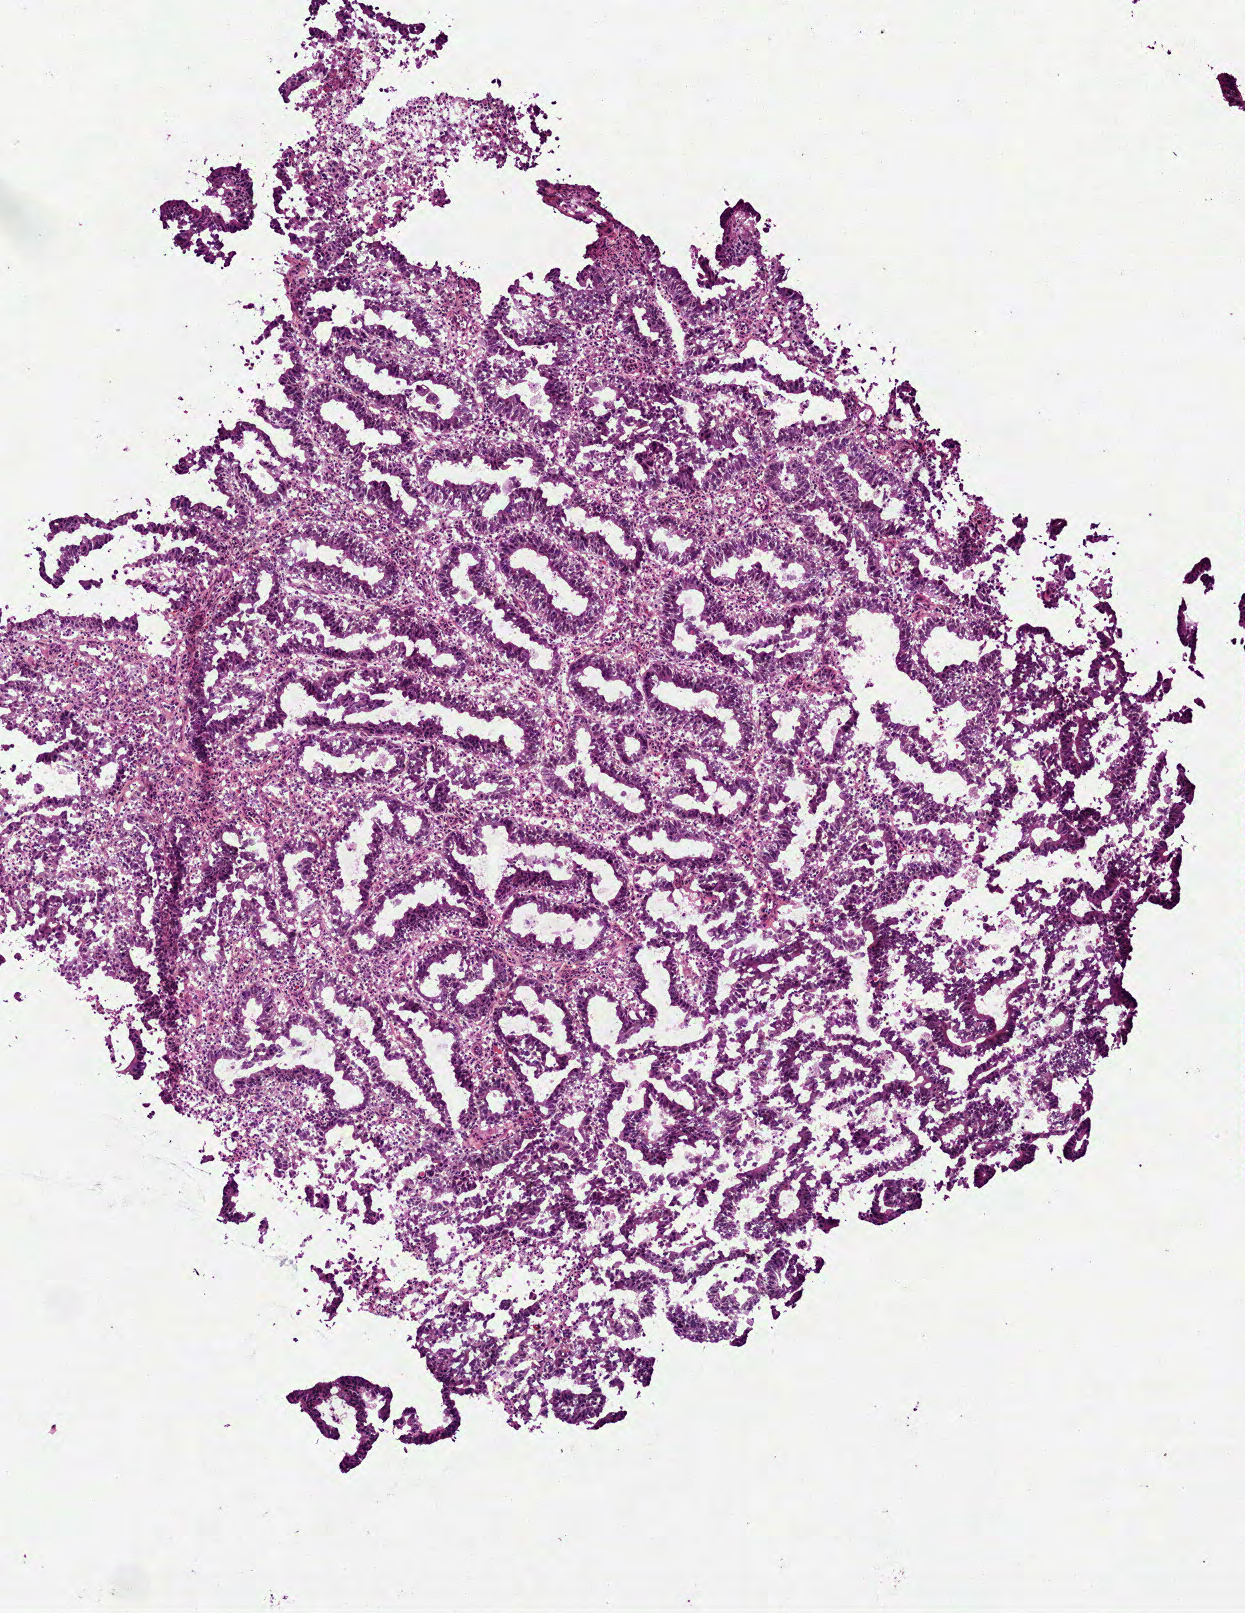
Whole-slide histology image, H&E-stained — shown as a low-resolution overview of the whole scanned area (about 2.5 x 3.3 mm, from a 40x scan), frozen section from the top of the tissue portion, sample: primary tumour, rectum. Patient: male, age at initial diagnosis 44 years. Composition of this section per pathologist review: tumour cells 85%, tumour nuclei 65%, normal cells 0%, stromal cells 15%, necrosis 5%.
Histologic diagnosis: Adenocarcinoma, NOS. AJCC pathologic stage: I (7th edition).